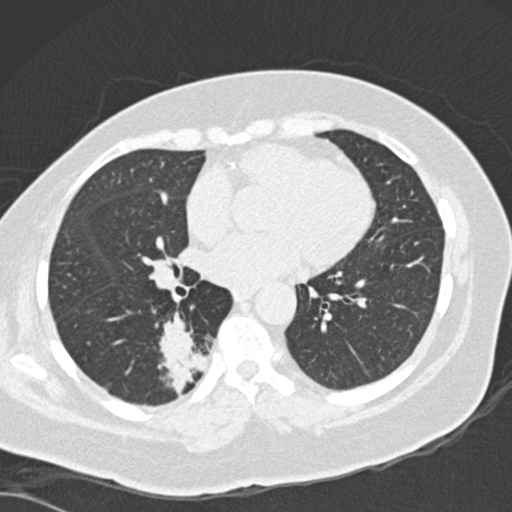
Low-dose screening chest CT, one axial slice. Position 71 of 162 along the scan axis. Reconstruction kernel B30f. Lung window (W 1500 / L -600 HU). 2 mm slice thickness. 512 × 512 image matrix, field of view 328 × 328 mm.
Outlined on this slice (manually delineated by an expert):
- lesion 1 (tumor, lower lobe of right lung): bounding box [x1, y1, x2, y2] px = [158, 311, 206, 396]